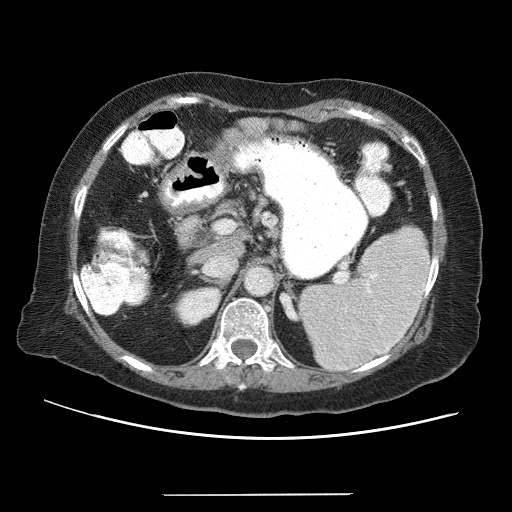
Contrast-enhanced abdominal CT (liver protocol), one axial slice. Slice 29 of 65 in the series (ordered by position). Soft-tissue window (W 400 / L 40 HU). 512 × 512 image matrix, field of view 380 × 380 mm. Case-level facts recorded for this patient, not image findings: diagnosis: hepatocellular carcinoma (patient treated with transarterial chemoembolisation; whether this scan precedes or follows treatment is not stated here); TNM stage (as recorded): Stage-IIIB; Child-Pugh class: A; tumour differentiation: moderately differentiated.
Outlined on this slice (semi-automatic segmentation, software-assisted and operator-edited):
- liver parenchyma outside the tumour (the mass and vessels are separate outlines, so this box may not span the whole liver): bounding box (x1, y1, x2, y2) in pixels: (208, 116, 296, 158)
- liver vessels: (240, 131, 256, 145)